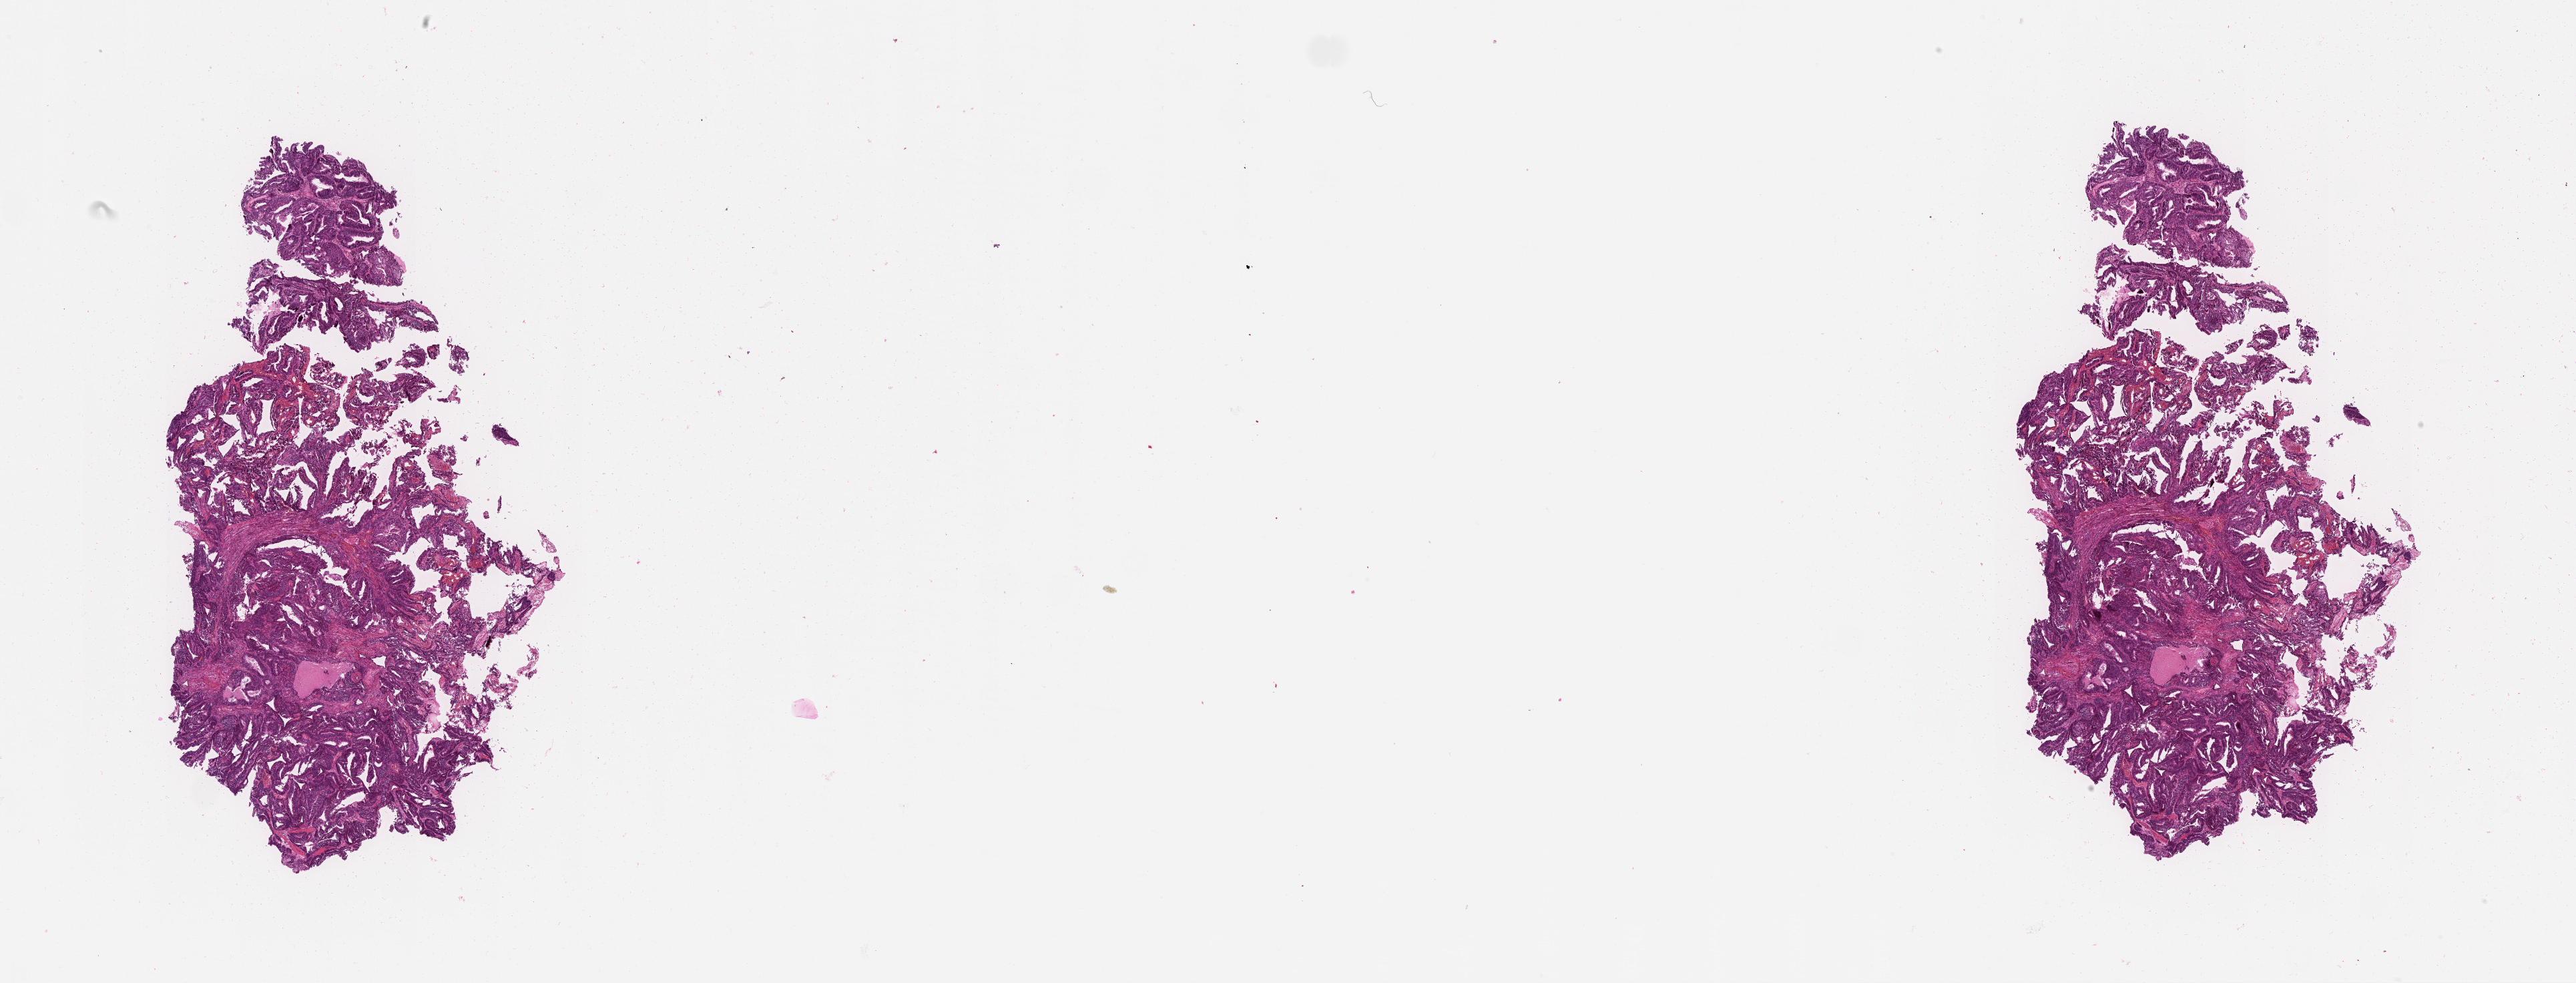
H&E-stained whole-slide image — a low-resolution overview of the entire scanned area, about 31.1 x 11.9 mm (from a 20x scan); tumour tissue sample, uterus. Patient: female, age 44 years. Histologic grade: G2 (moderately differentiated).
Diagnosis: Endometrioid adenocarcinoma, NOS.